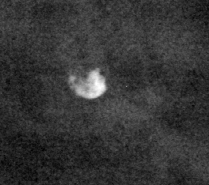
Cropped region of a digitized screen-film mammogram centred on a radiologist-marked abnormality; left breast; CC view; BI-RADS breast density category 2 (scale 1–4).
Finding: calcifications, morphology lucent center; BI-RADS assessment category 2; subtlety rating 5 on a 1 (subtle) to 5 (obvious) scale; benign without callback (not worked up further).